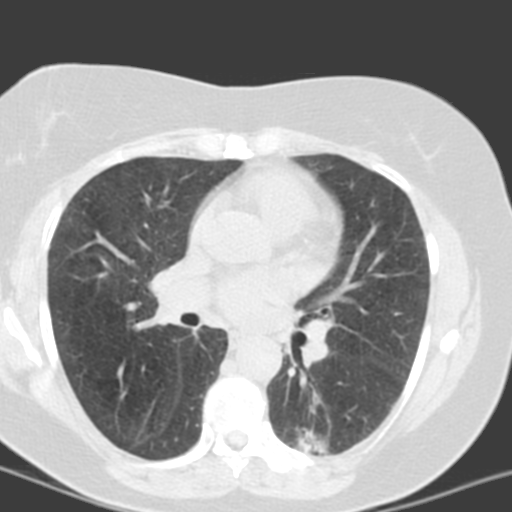
Axial slice from a low-dose chest CT screening exam; third annual screen; lung window (W 1500 / L -600 HU); 3.2 mm slice thickness; 120 kVp; slice 63 of 150 in the series; 512 × 512 image matrix, field of view 290 × 290 mm. Female, age 55 years at enrolment.
Lesion marked by an expert reader, bounding box (x1, y1, x2, y2) in pixels: (284, 410, 363, 463). The screening reader recorded 6 non-calcified nodules or masses ≥4 mm on this exam (left lower lobe, left lower lobe, left upper lobe, lingula, lingula, right middle lobe); which of them this box marks is not recorded. Official screen result: positive, no significant change: stable abnormalities potentially related to lung cancer, unchanged since the prior screening exam. Later outcome: lung cancer diagnosed 357 days after this screen — adenocarcinoma with mixed subtypes, left lower lobe, poorly differentiated (G3), stage IA (AJCC 6th edition), 21 mm at pathology.